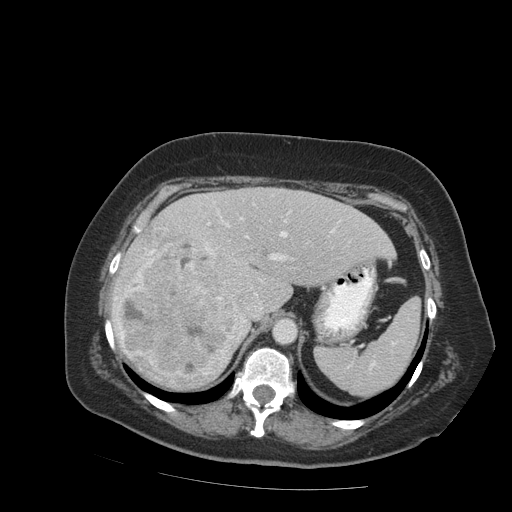
Contrast-enhanced abdominal CT (liver protocol), one axial slice; position 59 of 99 along the scan axis; reconstruction kernel STANDARD; 140 kVp; soft-tissue window (W 400 / L 40 HU); 512 × 512 image matrix, field of view 400 × 400 mm. From the clinical record (not read from this slice): diagnosis: hepatocellular carcinoma (patient treated with transarterial chemoembolisation; whether this scan precedes or follows treatment is not stated here); TNM stage (as recorded): Stage-IVB; Child-Pugh class: A; tumour nodularity: uninodular.
Structures marked on this image (semi-automatic segmentation, software-assisted and operator-edited):
- liver parenchyma outside the tumour (the mass and vessels are separate outlines, so this box may not span the whole liver): bounding box <112,187,394,390> (left, top, right, bottom; pixels)
- mass: <115,225,247,389>
- liver vessels: <206,202,340,310>